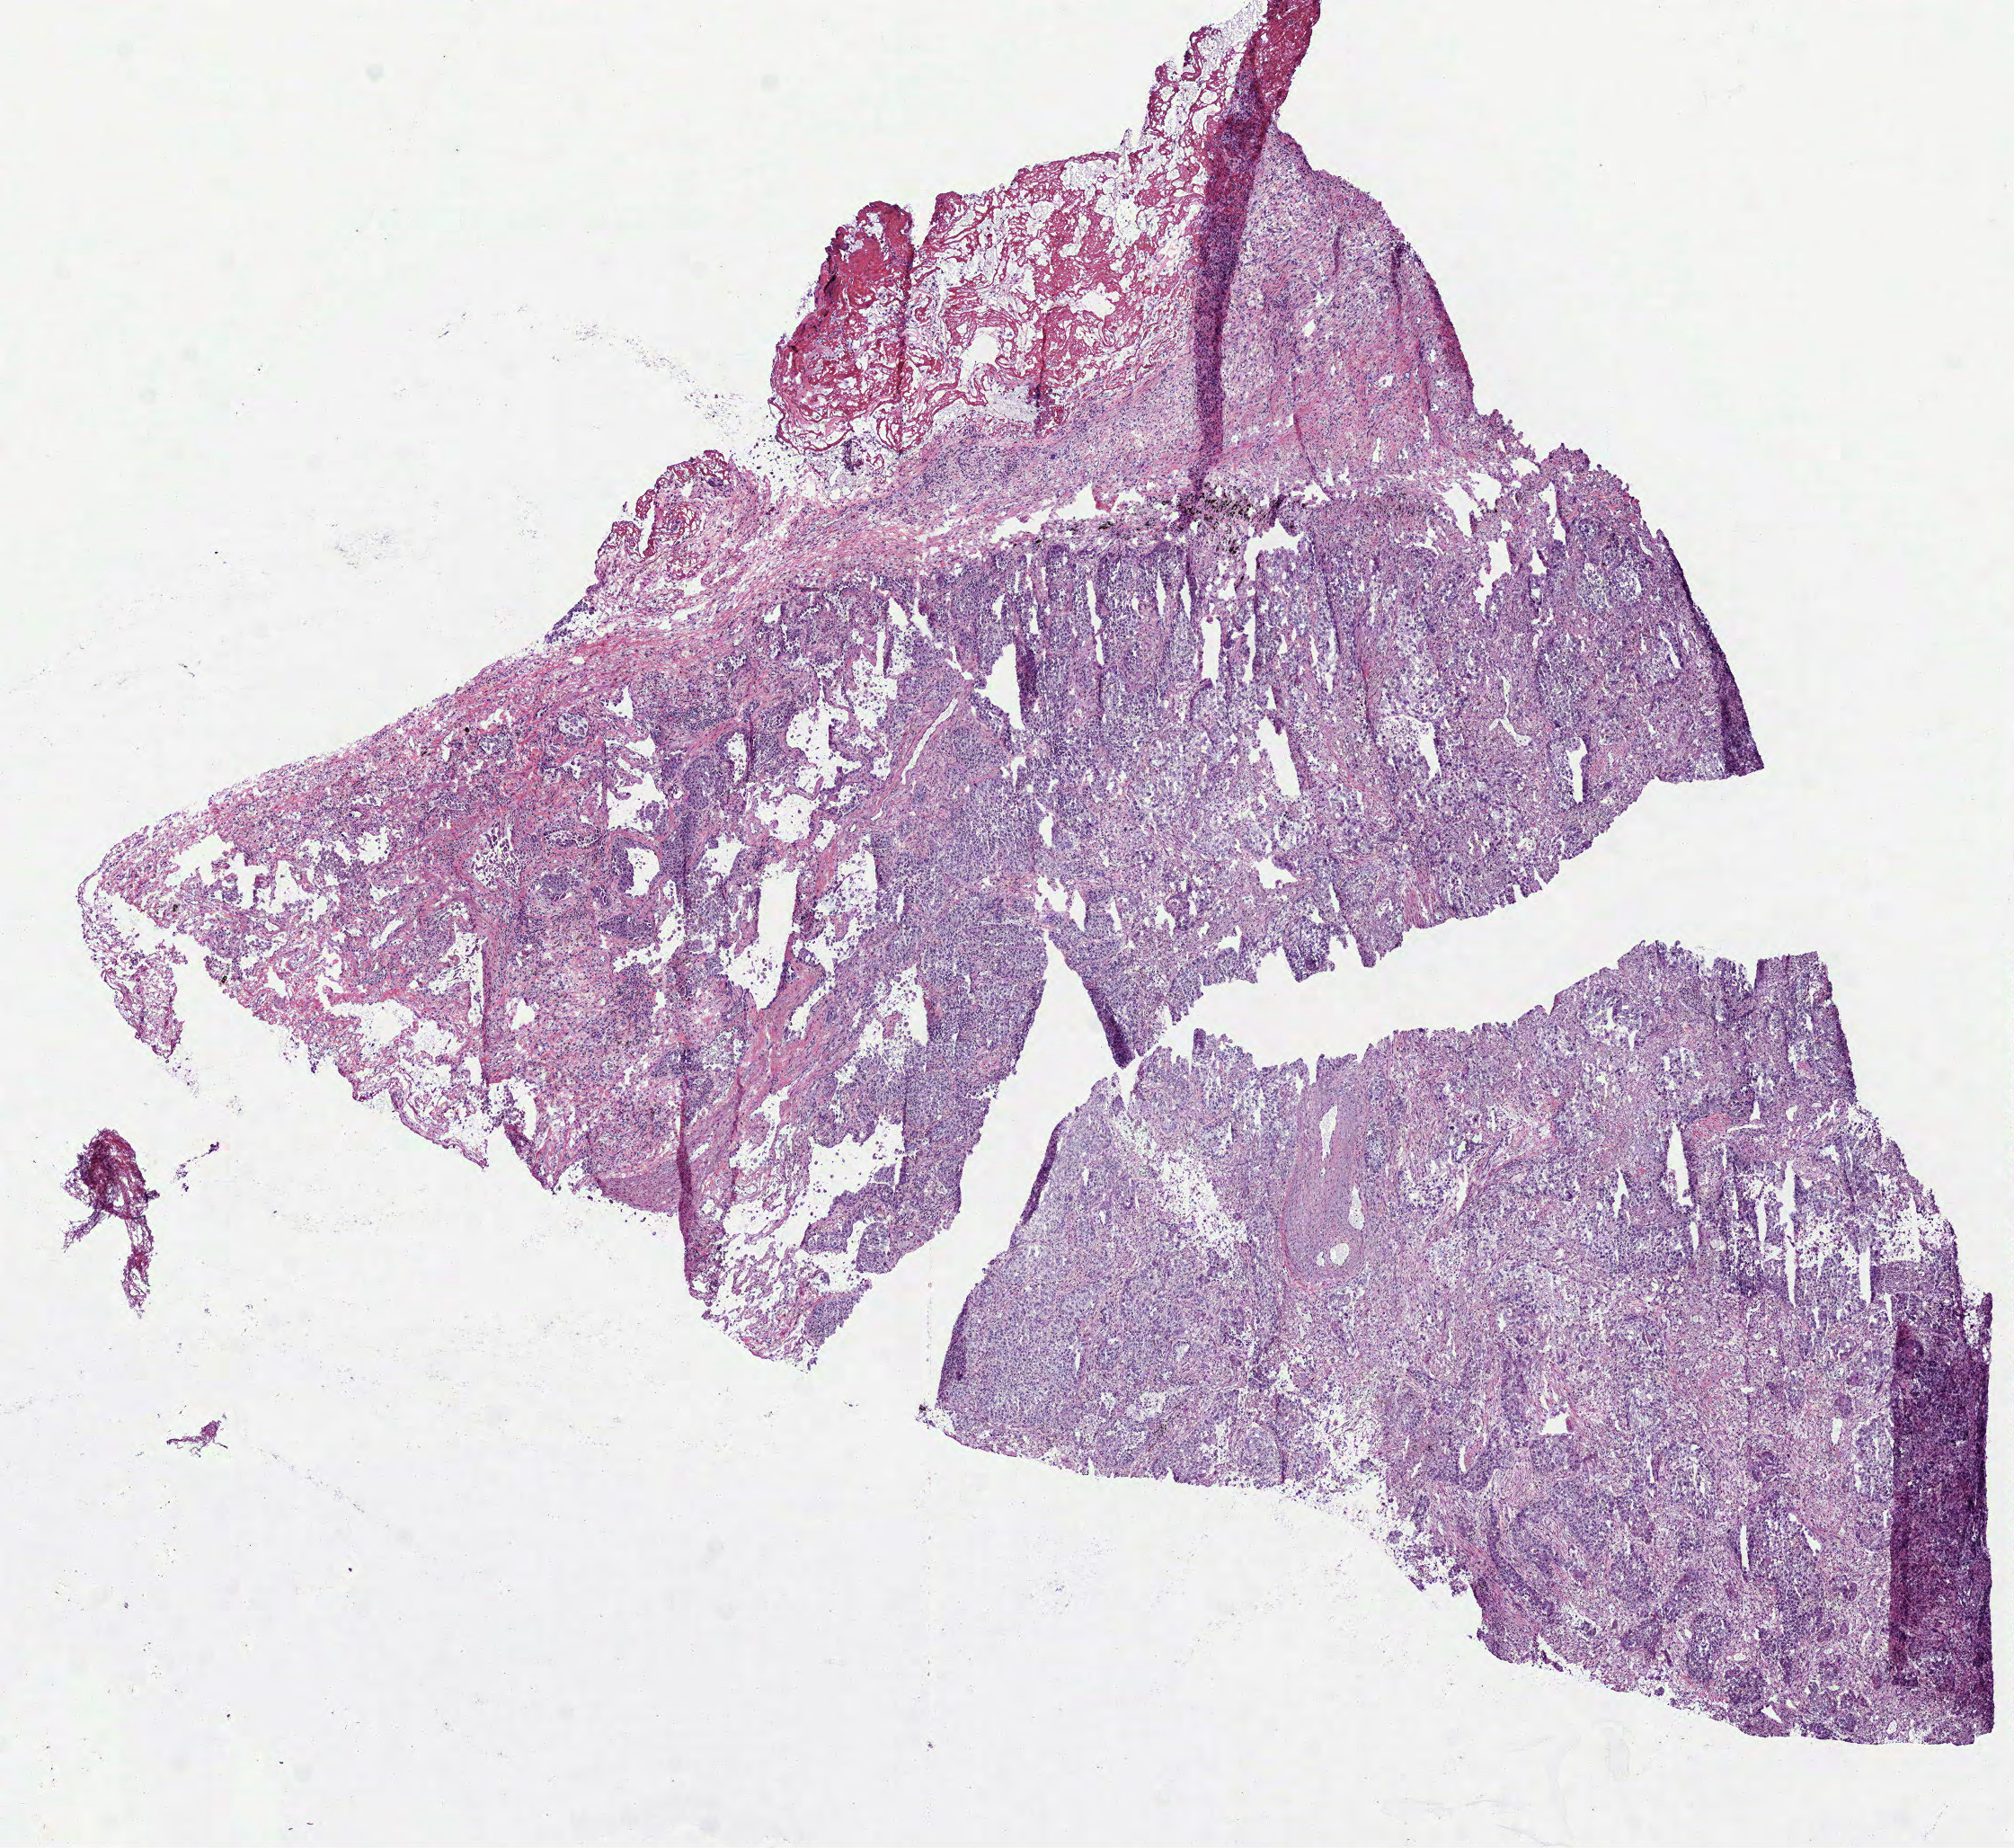
Digitized H&E tissue section (whole slide), a low-resolution overview of the entire scanned area, about 9.0 x 8.3 mm (from a 40x scan). Frozen section. Sample: primary tumour, lung. Male patient; age at initial diagnosis 70 years. Pathologist review of this section (percent, as recorded): tumour cells 73%, tumour nuclei 61%, normal cells 12%, stromal cells 15%, necrosis 0%. Inflammatory infiltration, as recorded: lymphocyte infiltration 10%, monocyte infiltration 5%, neutrophil infiltration 5%.
Pathologic diagnosis: Squamous cell carcinoma, NOS (upper lobe, lung). AJCC pathologic stage: IB (7th edition). Laterality: right.